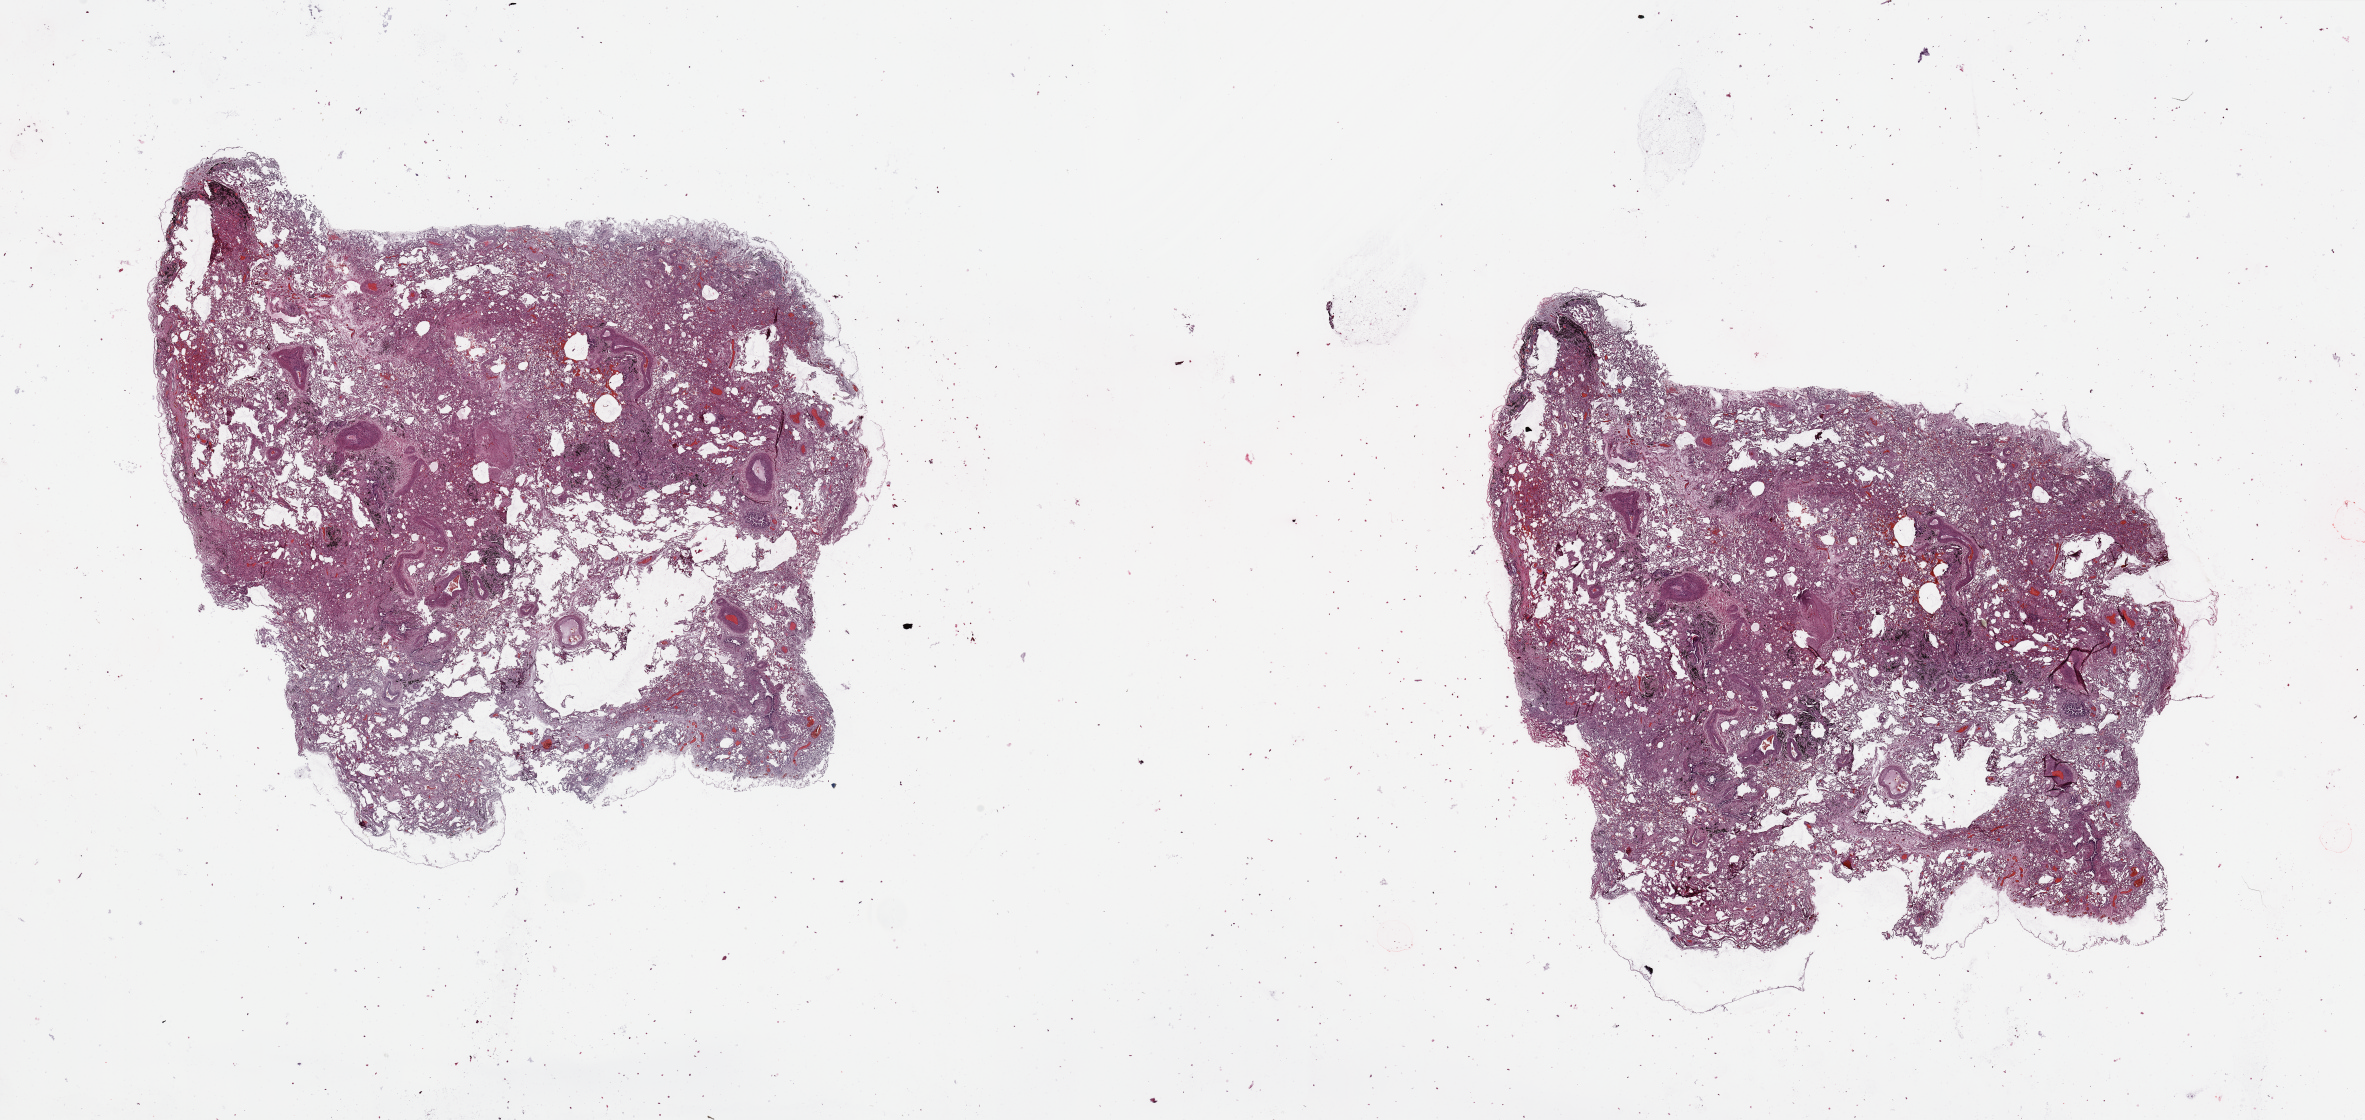
Whole-slide histology image, Hematoxylin and eosin (H&E) stained, a low-resolution overview of the entire scanned area, about 37.4 x 17.7 mm; normal (non-tumour) tissue sample, sampled site: lung. Male, 70 y/o.
This section: normal (non-tumour) tissue from the same patient. Patient diagnosis: Squamous cell carcinoma, NOS.